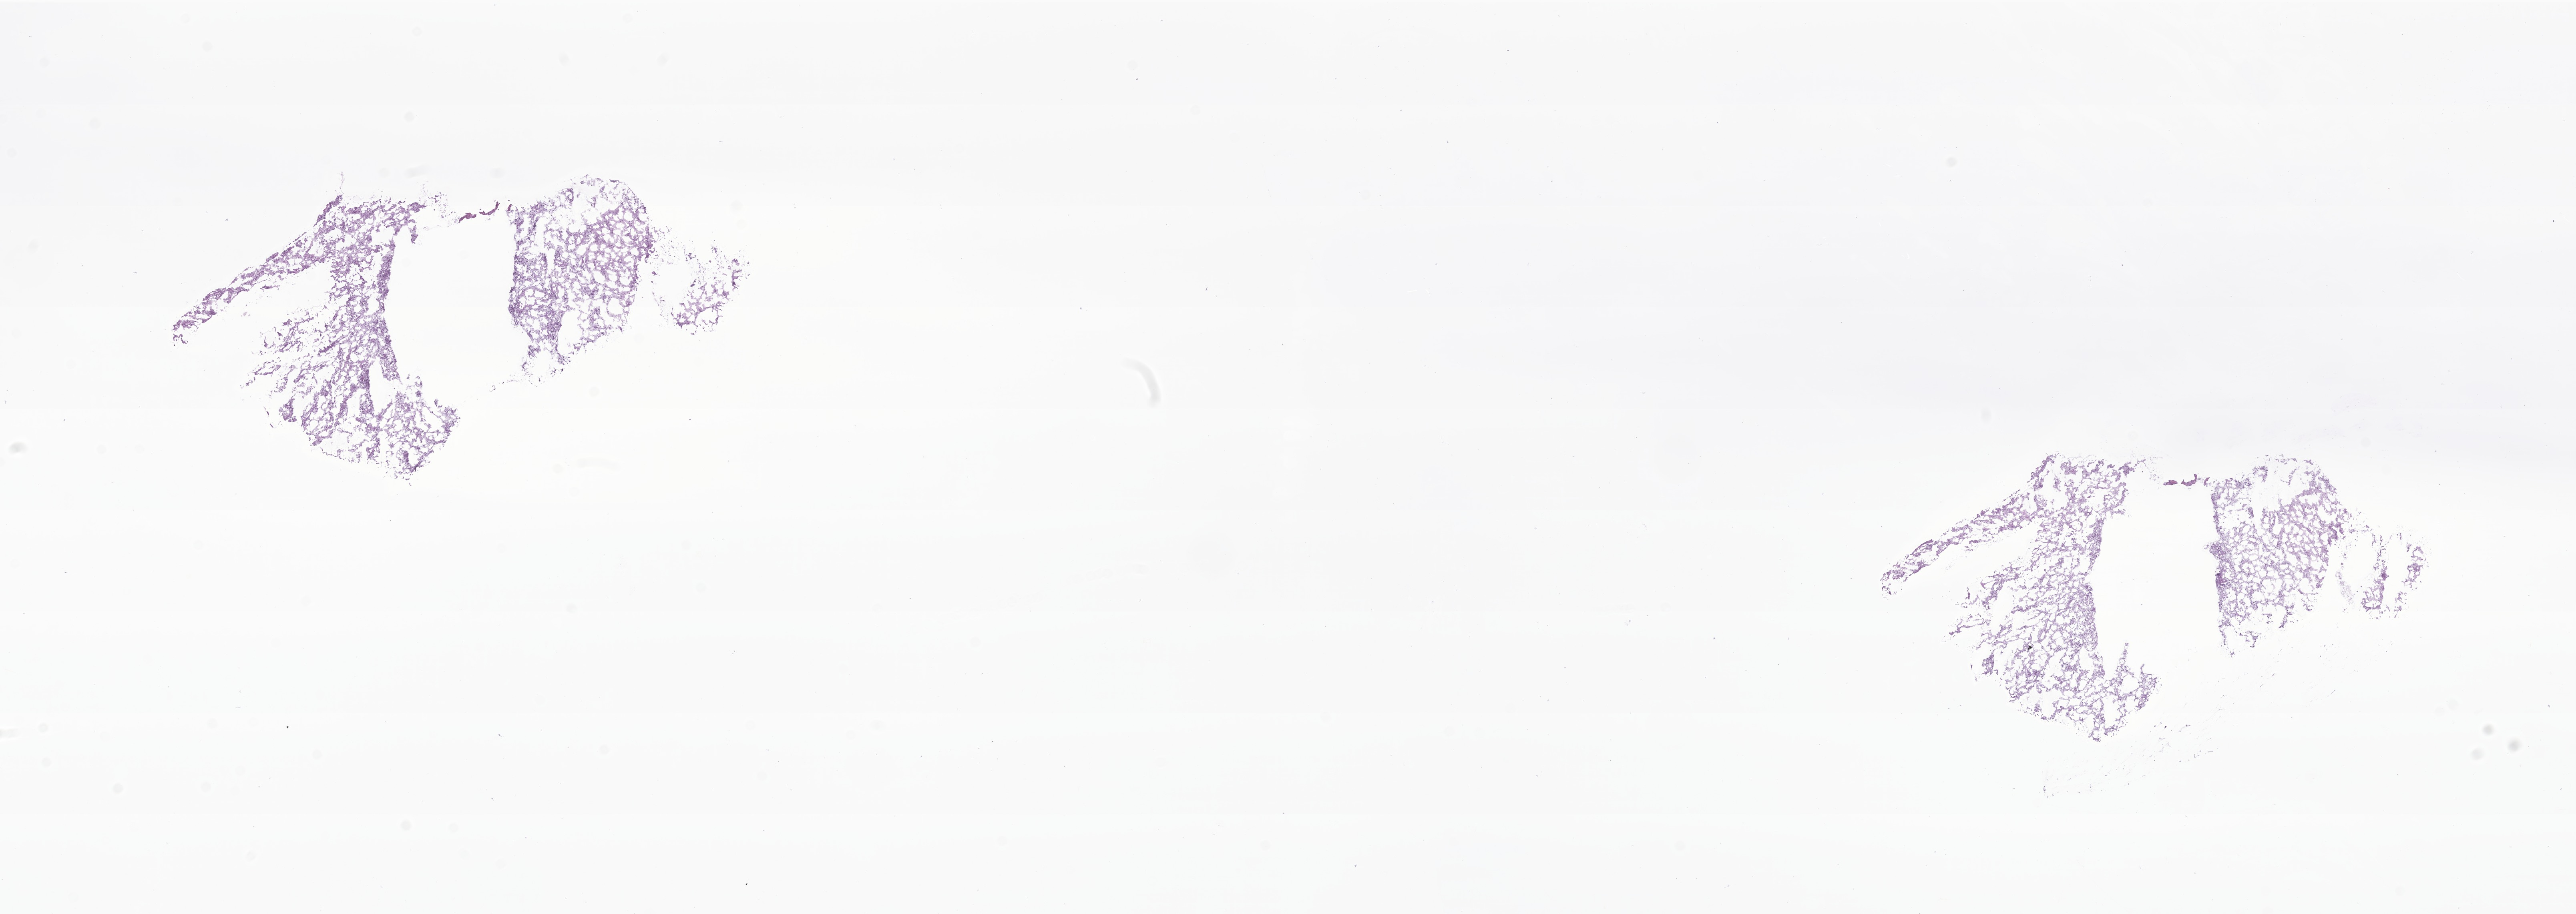
Whole-slide image, H&E stain of tumor tissue from the brain — shown as a low-resolution overview of the whole scanned area (about 27.1 x 9.6 mm), frozen section (OCT-embedded). Patient: male, age 111 months (9 years 3 months).
- diagnosis: Glioma, malignant